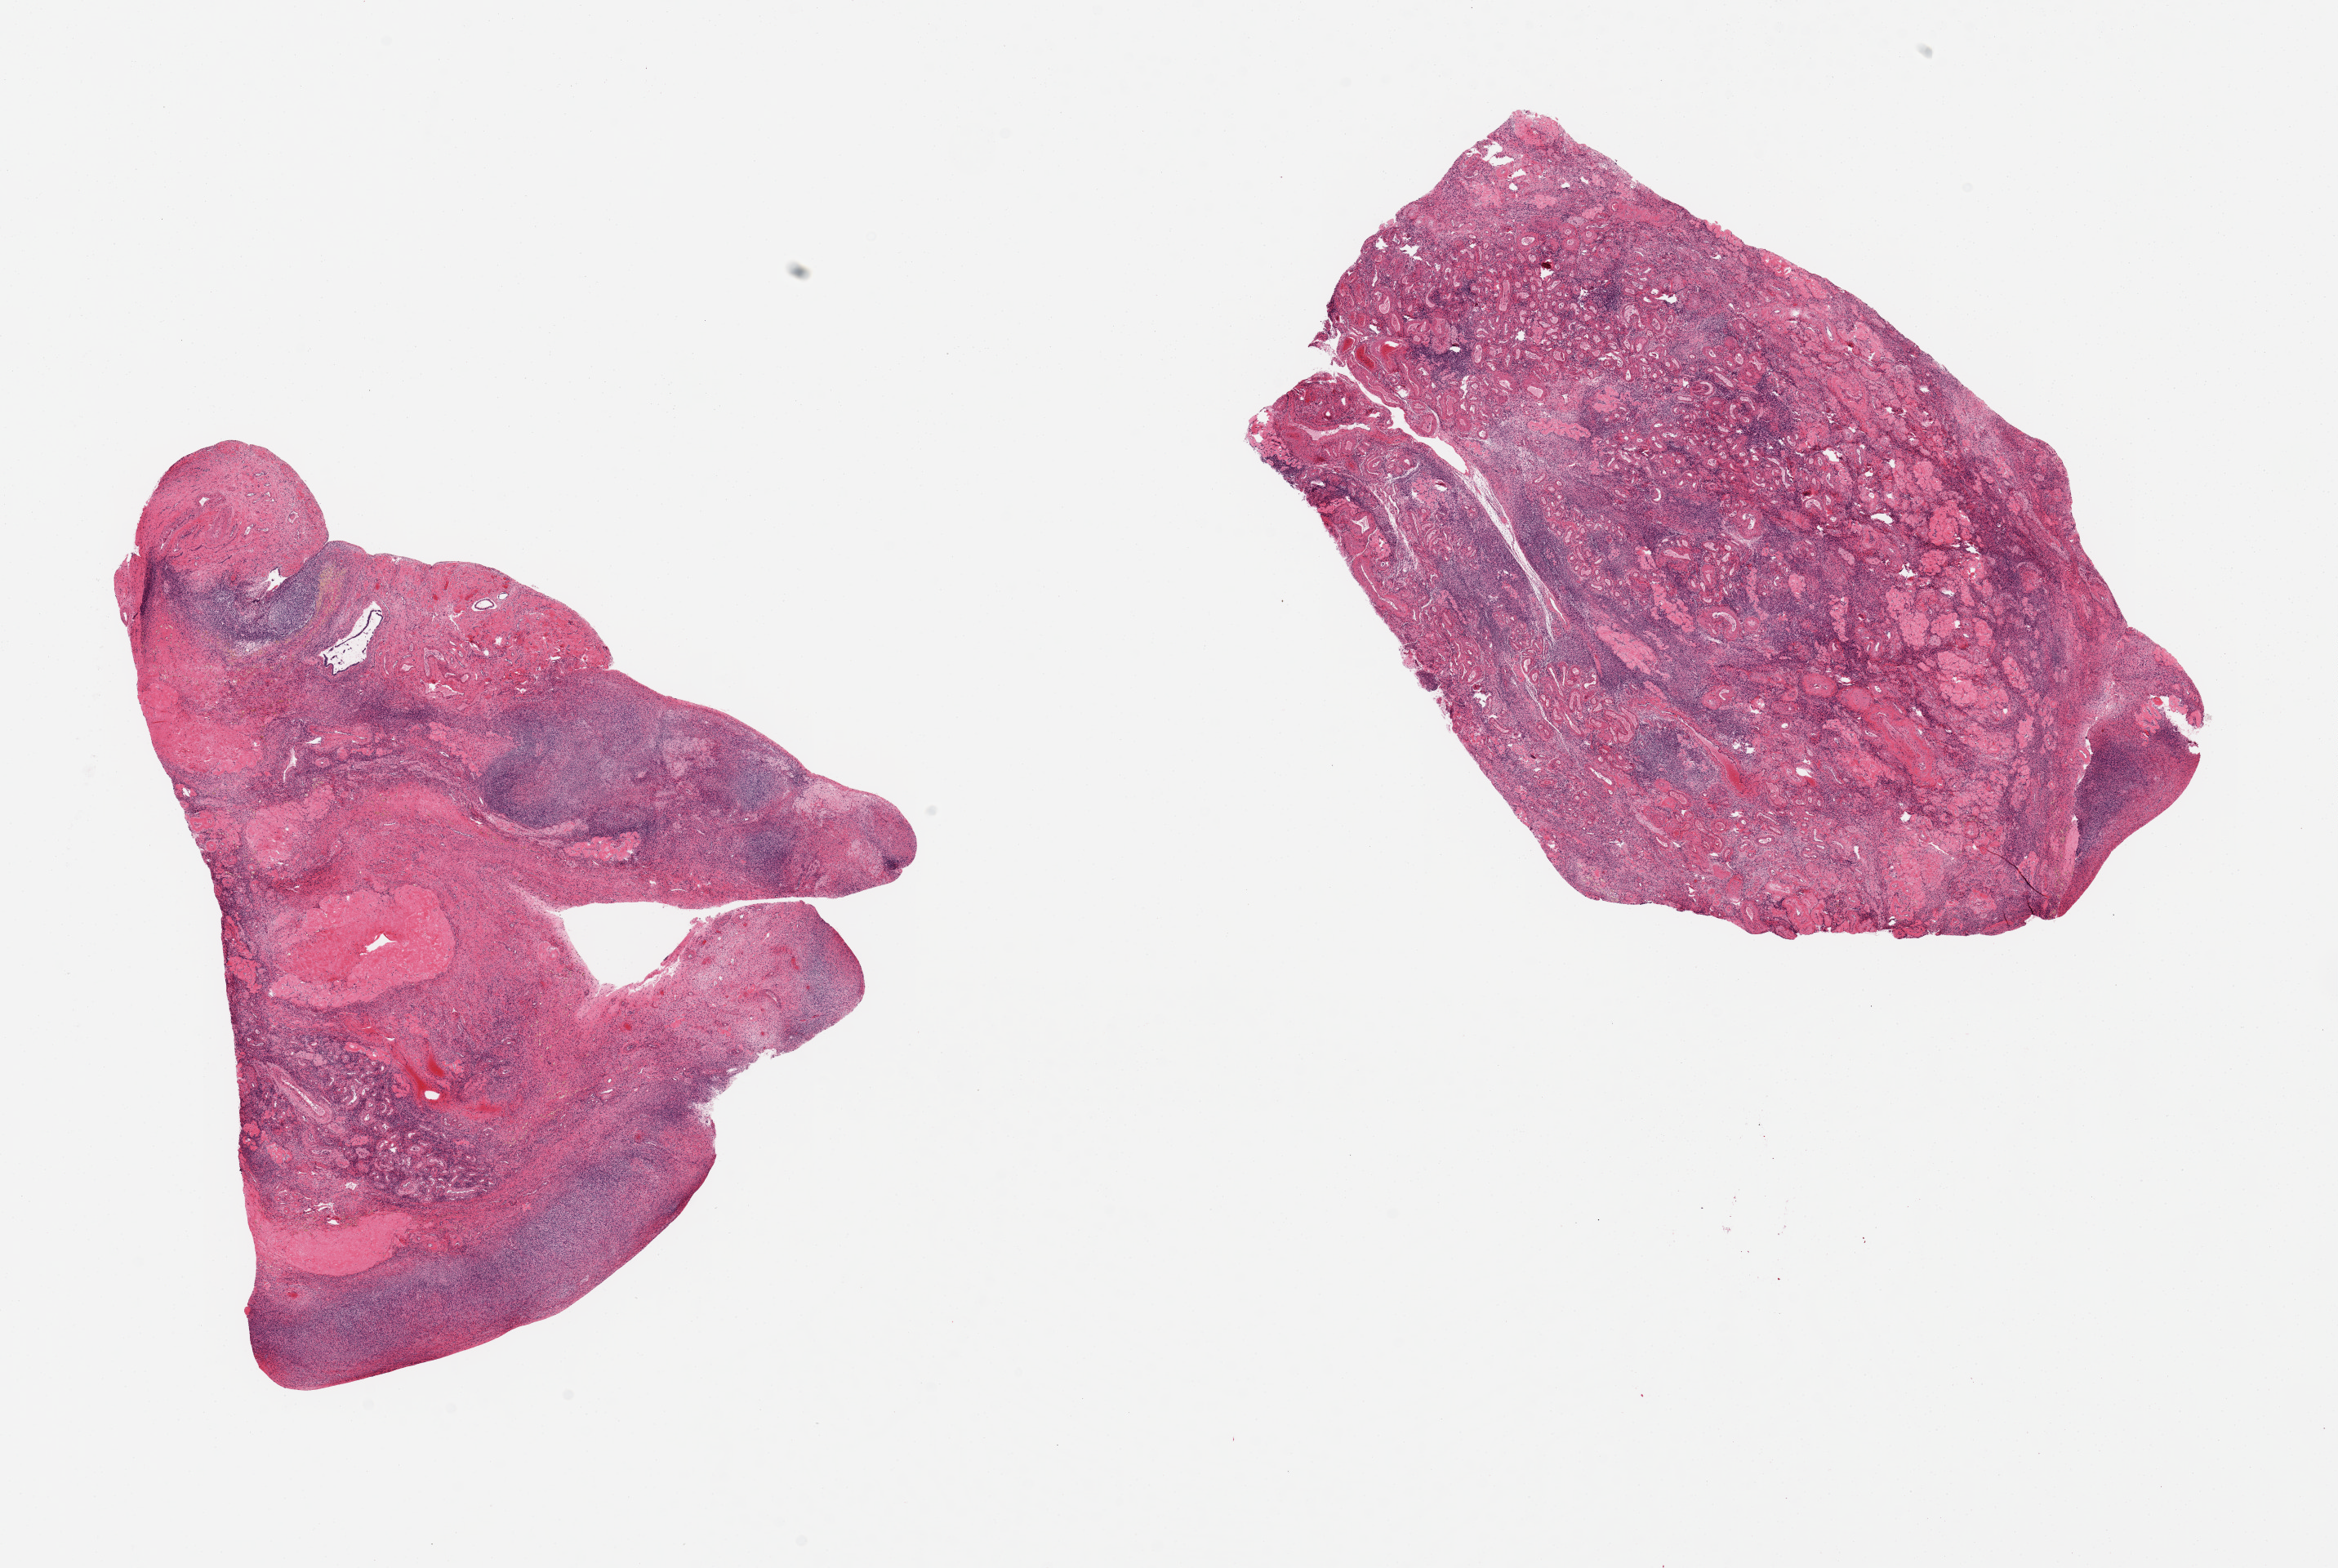
Hematoxylin and eosin (H&E) whole-slide image, brightfield — low-resolution overview of the scanned area, about 22.6 x 15.2 mm (from a 20x scan), PAXgene-fixed paraffin-embedded (PFPE) section, target tissue: ovary, donor tissue sample. Donor sex: female.
• reviewer comment on this tissue sample: 2 pieces, corpora albicantia/fibrosa and ovarian hilum